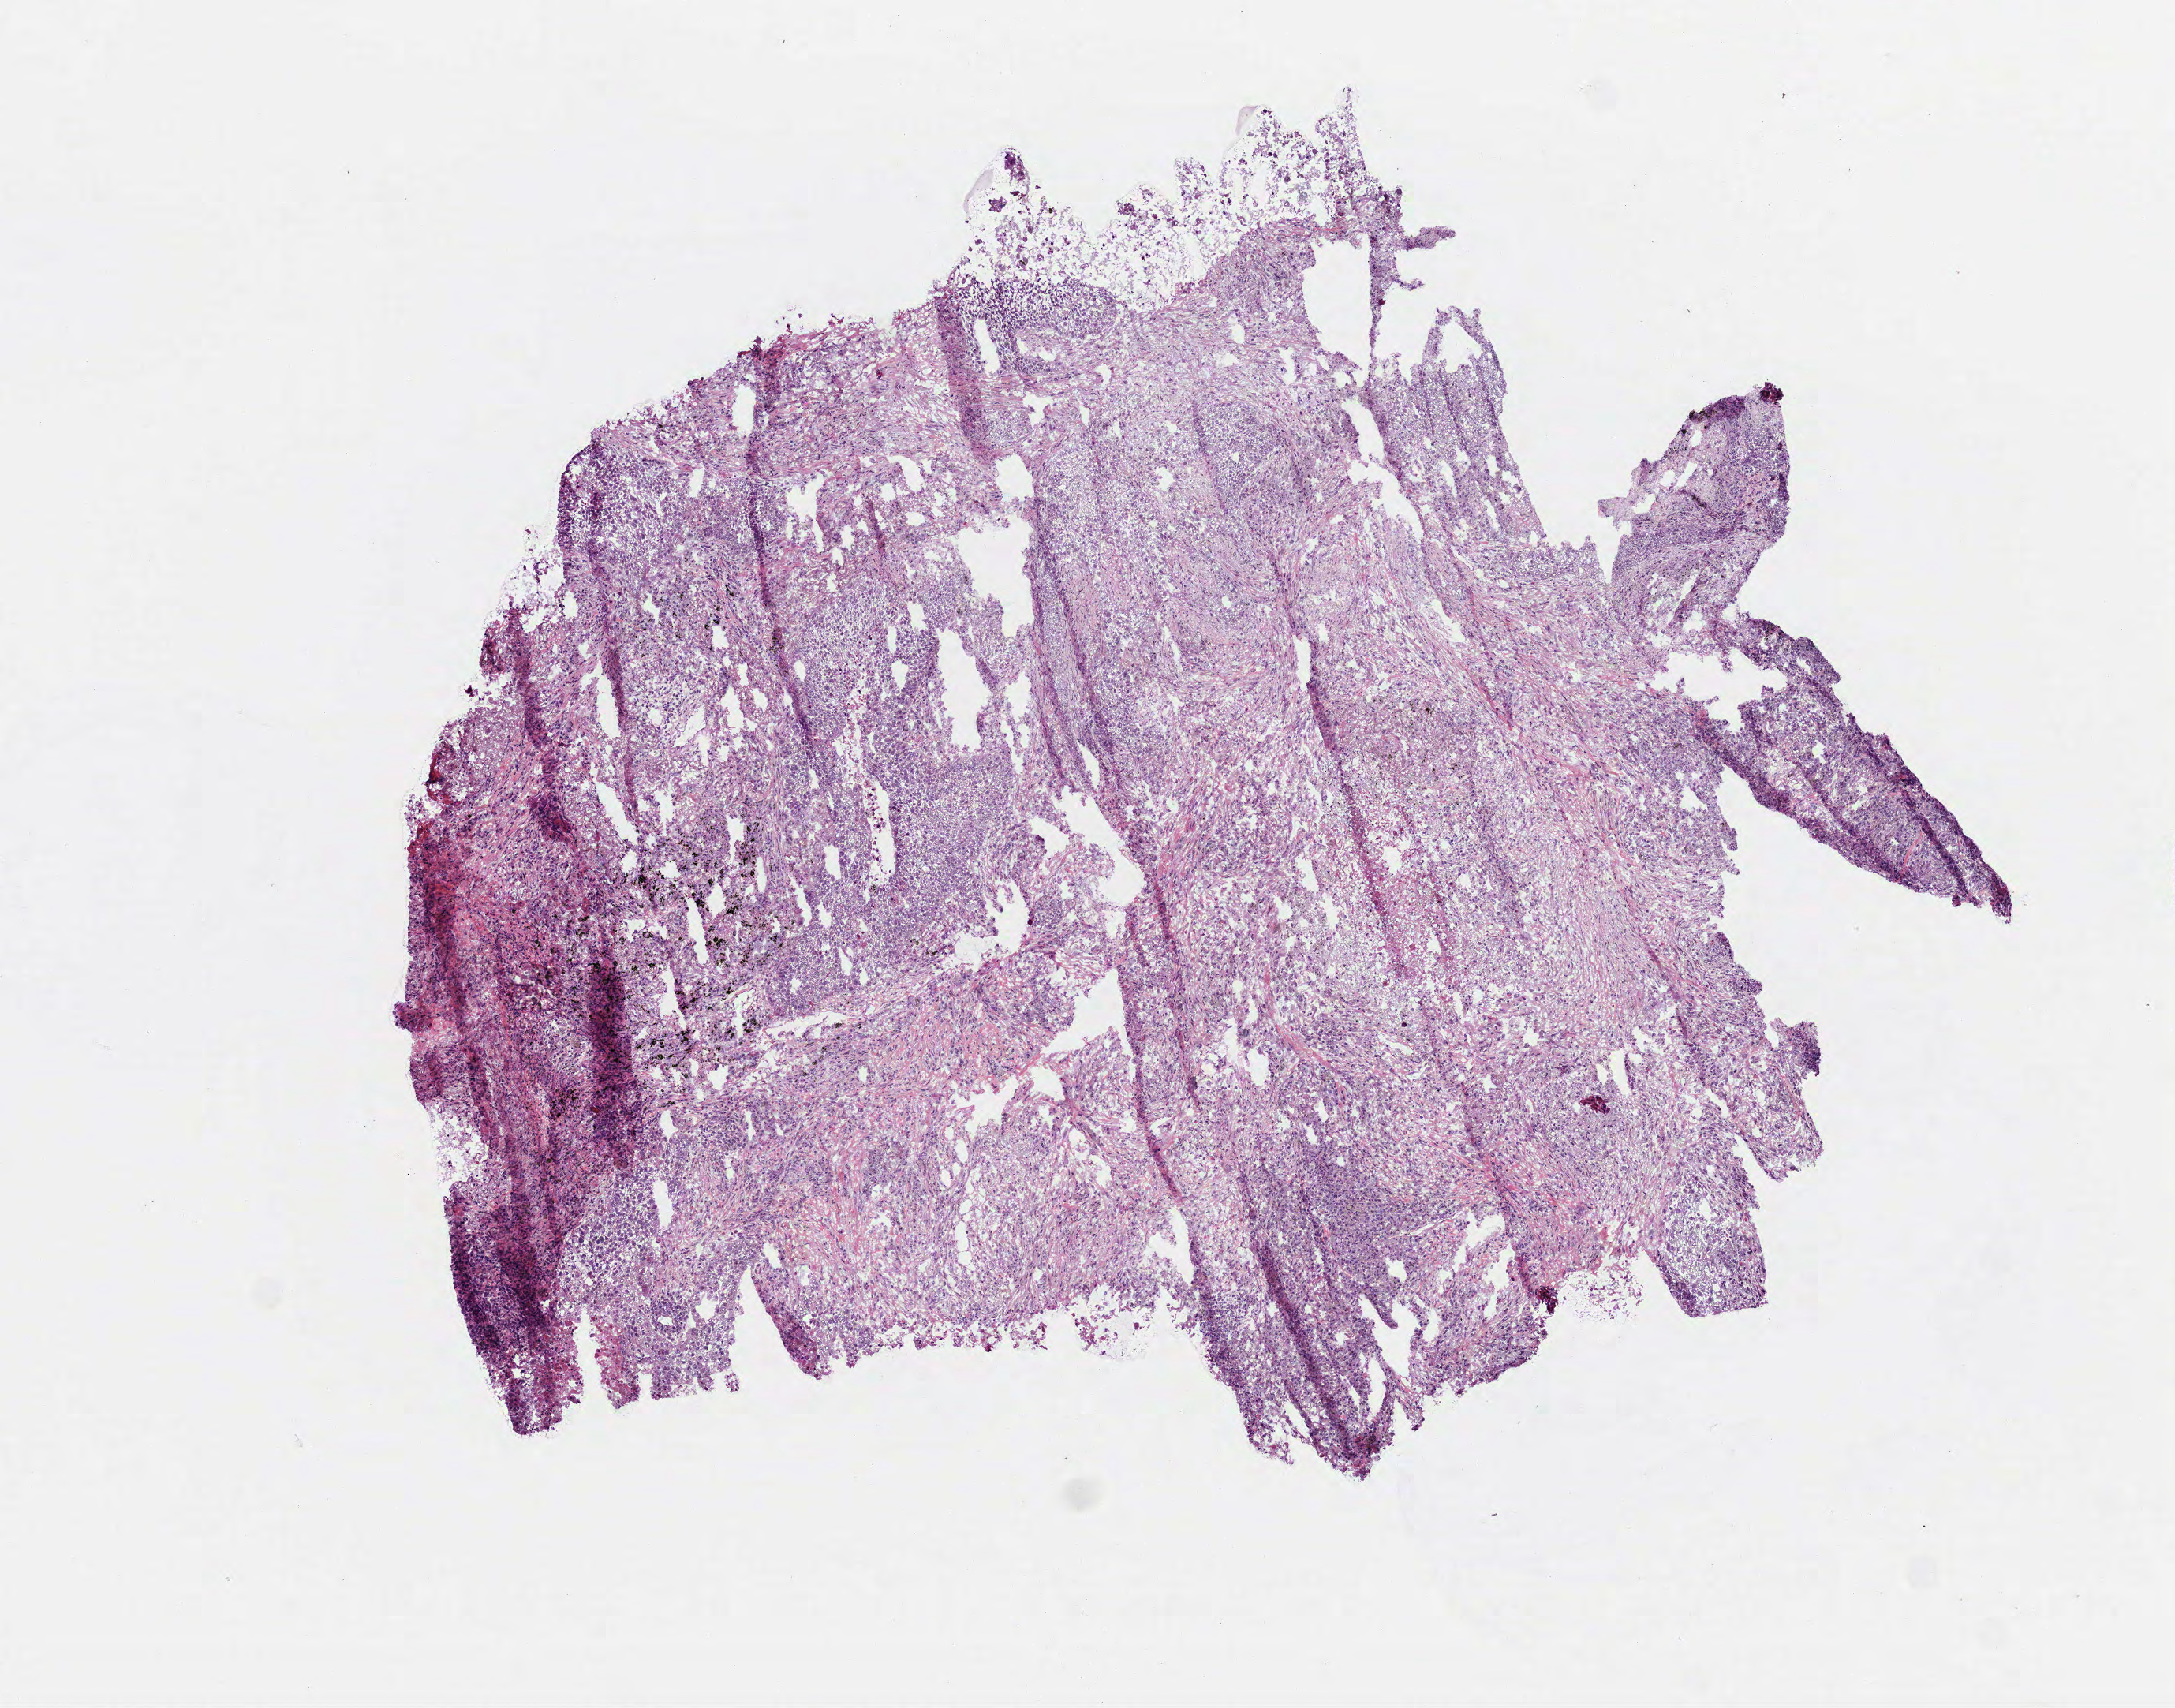
Digitized H&E-stained tissue section (whole slide), a low-resolution overview of the entire scanned area, about 5.6 x 4.4 mm (slide scanned at 40x), frozen section from the top of the tissue portion, lung, primary tumour sample. Patient sex: female. Composition of this section per pathologist review: tumour cells 78%, tumour nuclei 80%, normal cells 0%, stromal cells 20%, necrosis 2%. Infiltration values recorded for this section: lymphocyte infiltration 5%, monocyte infiltration 1%, neutrophil infiltration 2%.
AJCC pathologic stage: IA (6th edition). TNM: T1 N0 M0. Histologic diagnosis: Squamous cell carcinoma, NOS (upper lobe, lung).